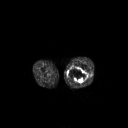
FDG PET of an extremity soft-tissue mass (from a PET/CT study), one axial slice; position 226 of 267 along the scan axis; 3.27 mm slice thickness; 128 × 128 image matrix, field of view 700 × 700 mm. Male patient, age 44 years. Case-level facts recorded for this patient, not image findings: histological type: undifferentiated pleomorphic liposarcoma; grade: high; site of the primary tumour: left thigh.
Annotated regions visible in this slice (expert contour drawn on MRI and transferred to this co-registered scan by the dataset authors):
- gross tumour volume including surrounding oedema: bounding box <67,67,87,83> (left, top, right, bottom; pixels)
- gross tumour volume (mass): <67,67,87,83>